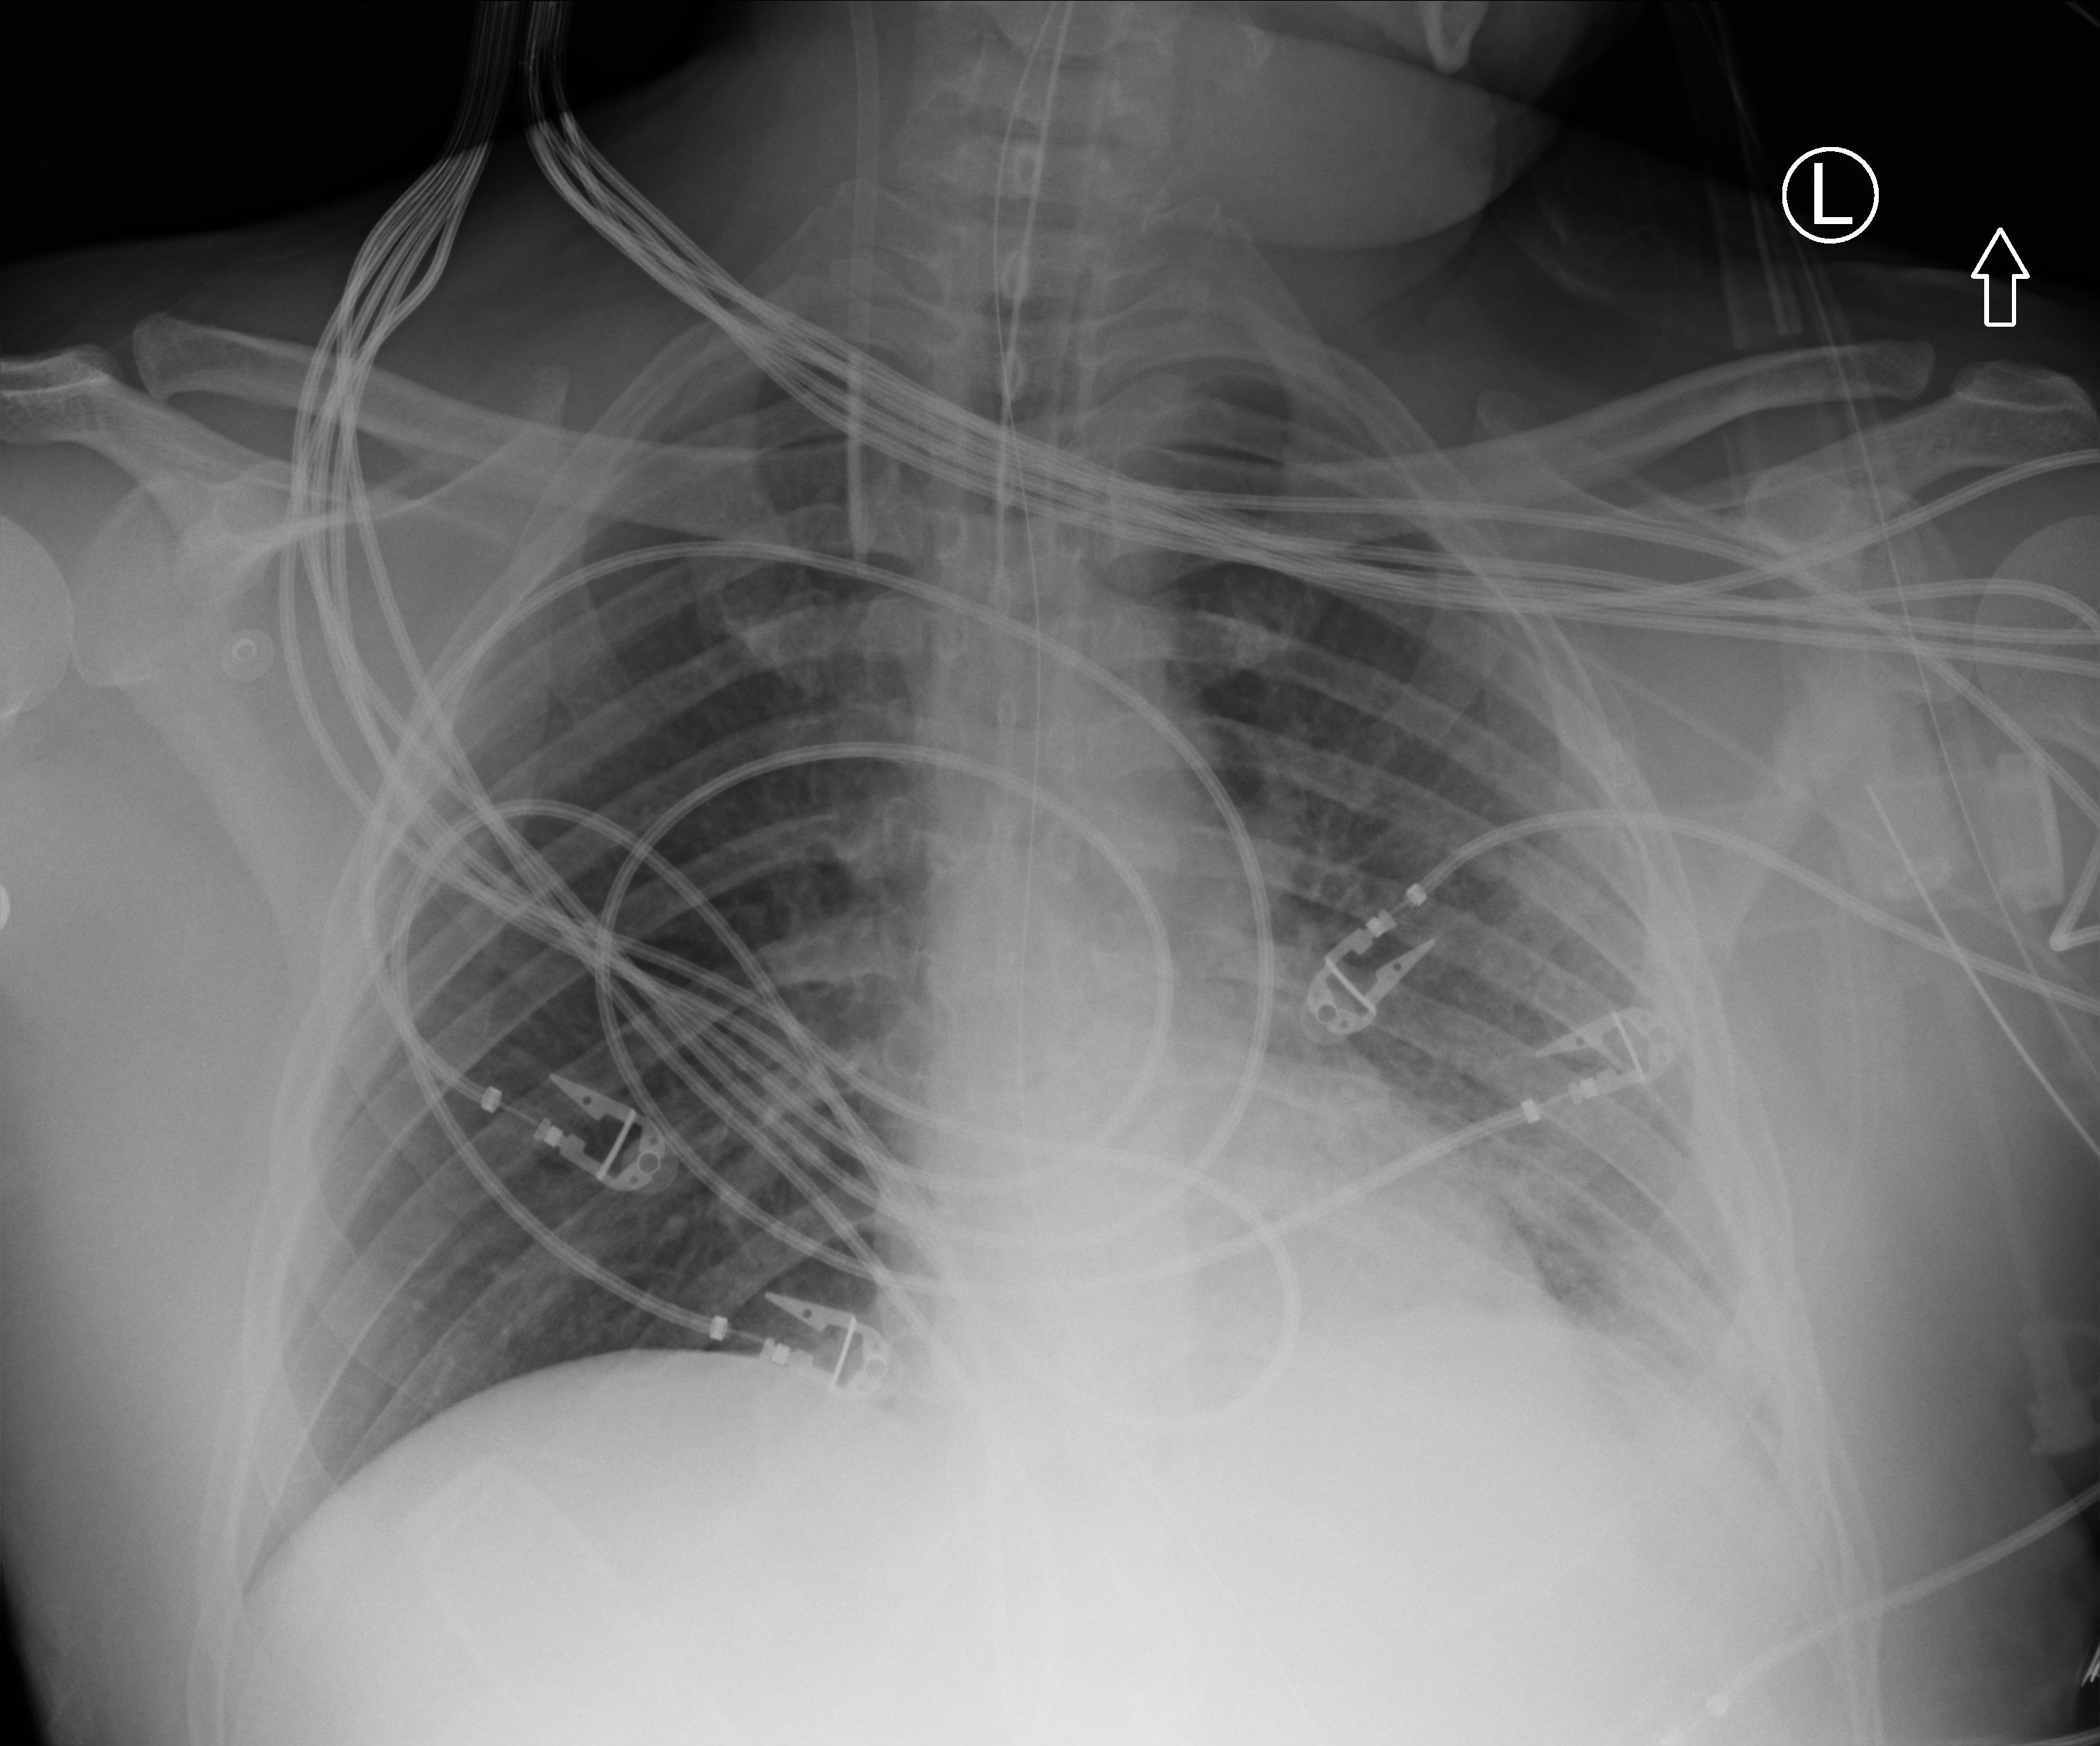
Chest X-ray (portable), anteroposterior (AP) projection. Adult patient hospitalised with COVID-19, age 18–59 years.
Hospital-stay facts (about this admission, not read from this image; timing relative to this image not recorded): mechanically ventilated during this hospital stay: yes; length of hospital stay: 19 days.